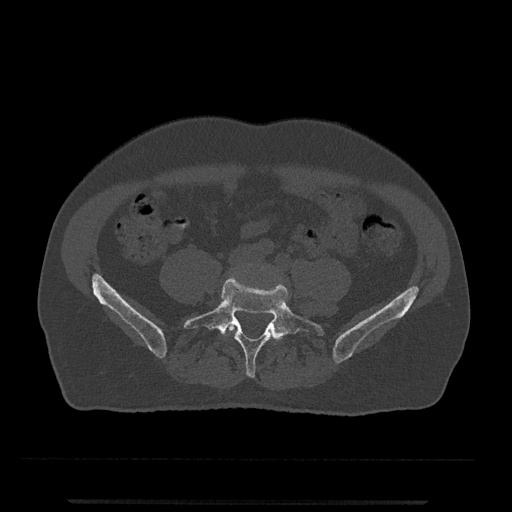
CT including the spine, one axial slice. Slice 83 of 797 in the series (ordered by position). 120 kVp. Bone window (W 1800 / L 400 HU). 0.5 mm slice thickness. 512 × 512 image matrix, field of view 419 × 419 mm. Male patient, age 63 years. Case-level facts recorded for this patient, not image findings: primary cancer: prostate.
Structures marked on this image (semi-automatic segmentation, software-assisted and operator-edited):
- L4 vertebra: bounding box (x1, y1, x2, y2) in pixels: (225, 322, 236, 333)
- L5 vertebra: (183, 274, 323, 378)